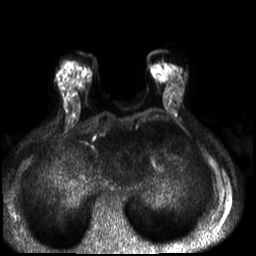
Breast MRI, one axial slice. Slice 8 of 30 in the series (ordered by position). Diffusion-weighted series; image 2 of 4 stored at this slice position (different b-values; order by instance number). 3 T. 256 × 256 image matrix, field of view 320 × 320 mm. Female patient.
Structures marked on this image (outlined manually by an expert reader):
- tumour on diffusion-weighted imaging: bounding box <81,70,91,77> (left, top, right, bottom; pixels)